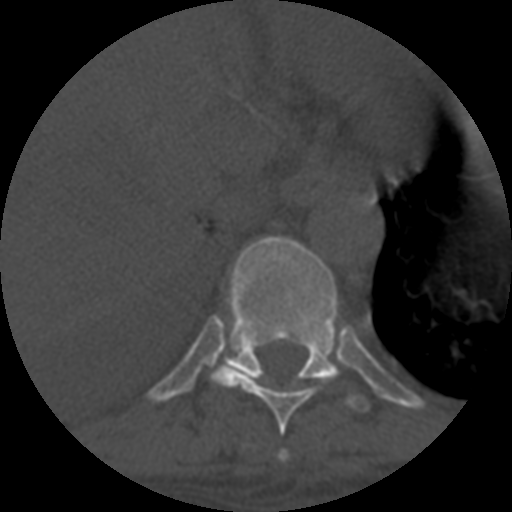
CT including the spine, one axial slice. Position 367 of 708 along the scan axis. Reconstruction kernel STANDARD. 120 kVp. One of 3 acquisitions stored at this slice position. Bone window (W 1800 / L 400 HU). 1.25 mm slice thickness. 512 × 512 image matrix, field of view 160 × 160 mm. Patient age 55 years. Case-level facts recorded for this patient, not image findings: primary cancer: colon; vertebrae with lytic lesions (as recorded): T12, L1, L5.
Structures marked on this image (semi-automatic segmentation, software-assisted and operator-edited):
- T10 vertebra: bounding box <224,236,368,410> (left, top, right, bottom; pixels)
- T8 vertebra: <279,450,288,462>
- T9 vertebra: <209,364,338,435>